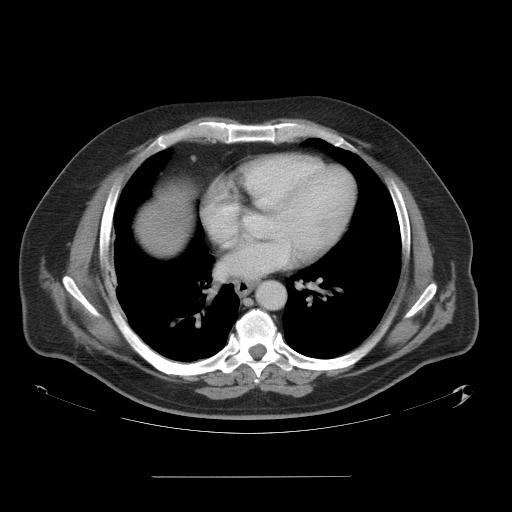
Contrast-enhanced abdominal CT, one axial slice. Position 56 of 58 along the scan axis. Intravenous contrast given. Soft-tissue window (W 400 / L 40 HU). 5 mm slice thickness. 512 × 512 image matrix. Male patient, age 63 years. Case-level facts recorded for this patient, not image findings: diagnosis: colorectal cancer liver metastases, imaged before liver resection; multiple liver metastases: no; largest metastasis: 4.2 cm.
Outlined on this slice (manually delineated by an expert):
- liver: bounding box <138,183,189,253> (left, top, right, bottom; pixels)
- planned liver remnant (the part of the liver to remain after resection): <139,230,181,254>